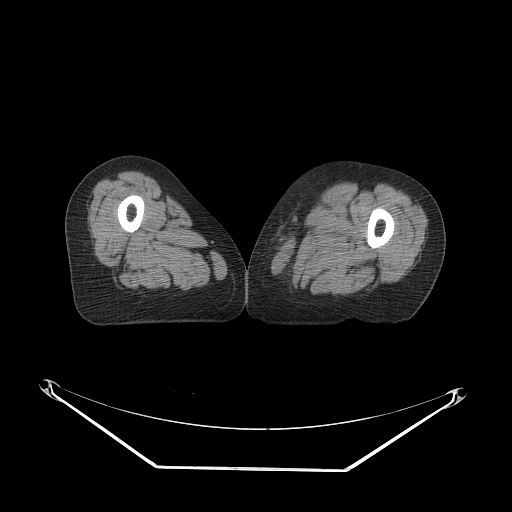
CT of an extremity soft-tissue mass (from a PET/CT study), one axial slice. Slice 52 of 91 in the series (ordered by position). Reconstruction kernel STANDARD. 140 kVp. Soft-tissue window (W 400 / L 40 HU). 512 × 512 image matrix, field of view 500 × 500 mm. Female patient. Case-level facts recorded for this patient, not image findings: histological type: pleomorphic leiomyosarcoma; grade: high; site of the primary tumour: left thigh.
Structures marked on this image (expert contour drawn on MRI and transferred to this co-registered scan by the dataset authors):
- gross tumour volume including surrounding oedema: bounding box [x1, y1, x2, y2] px = [272, 201, 323, 229]